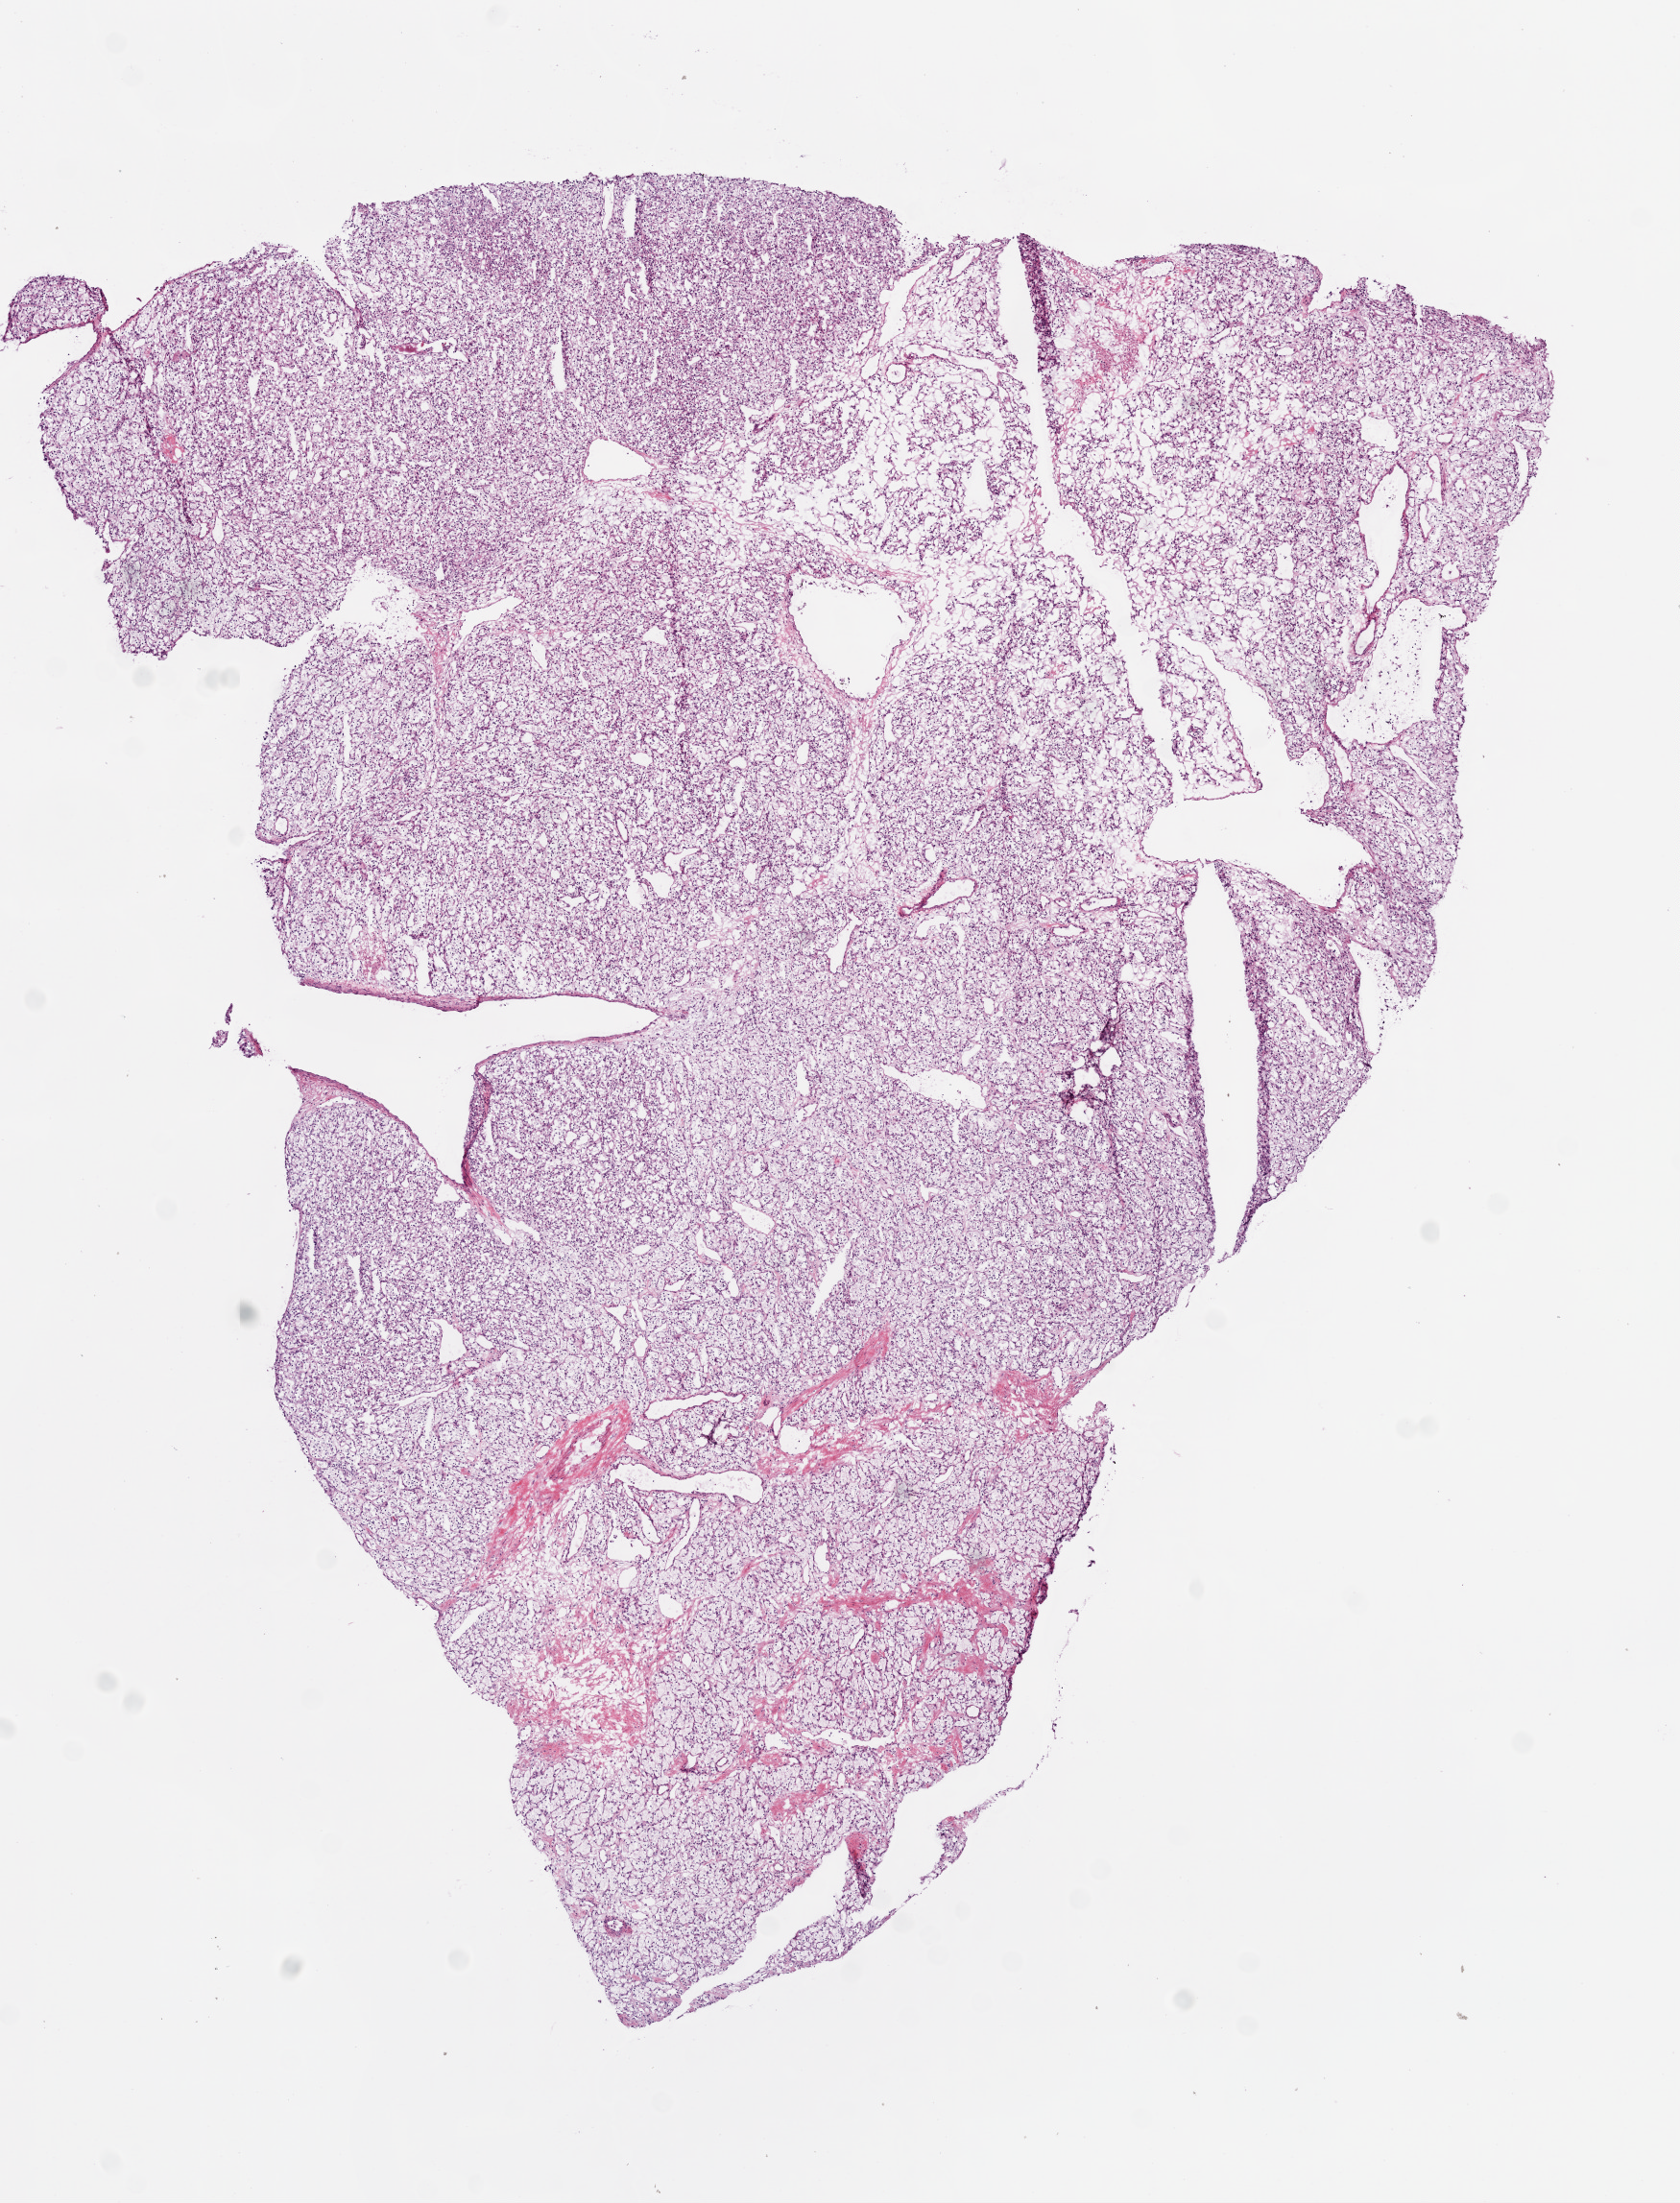
Whole-slide histology image, H&E, low-resolution overview of the scanned area, about 7.0 x 9.2 mm (acquisition: 20x scan); frozen section; kidney, primary tumour sample. Male, age 48 years at initial diagnosis. Histologic grade: G2 (moderately differentiated). Slide review estimates, as recorded: tumour cells 95%, tumour nuclei 99%, normal cells 0%, stromal cells 5%, necrosis 0%.
Diagnosis: Clear cell adenocarcinoma, NOS. Laterality: right. AJCC pathologic stage: I. TNM: T1a NX M0.